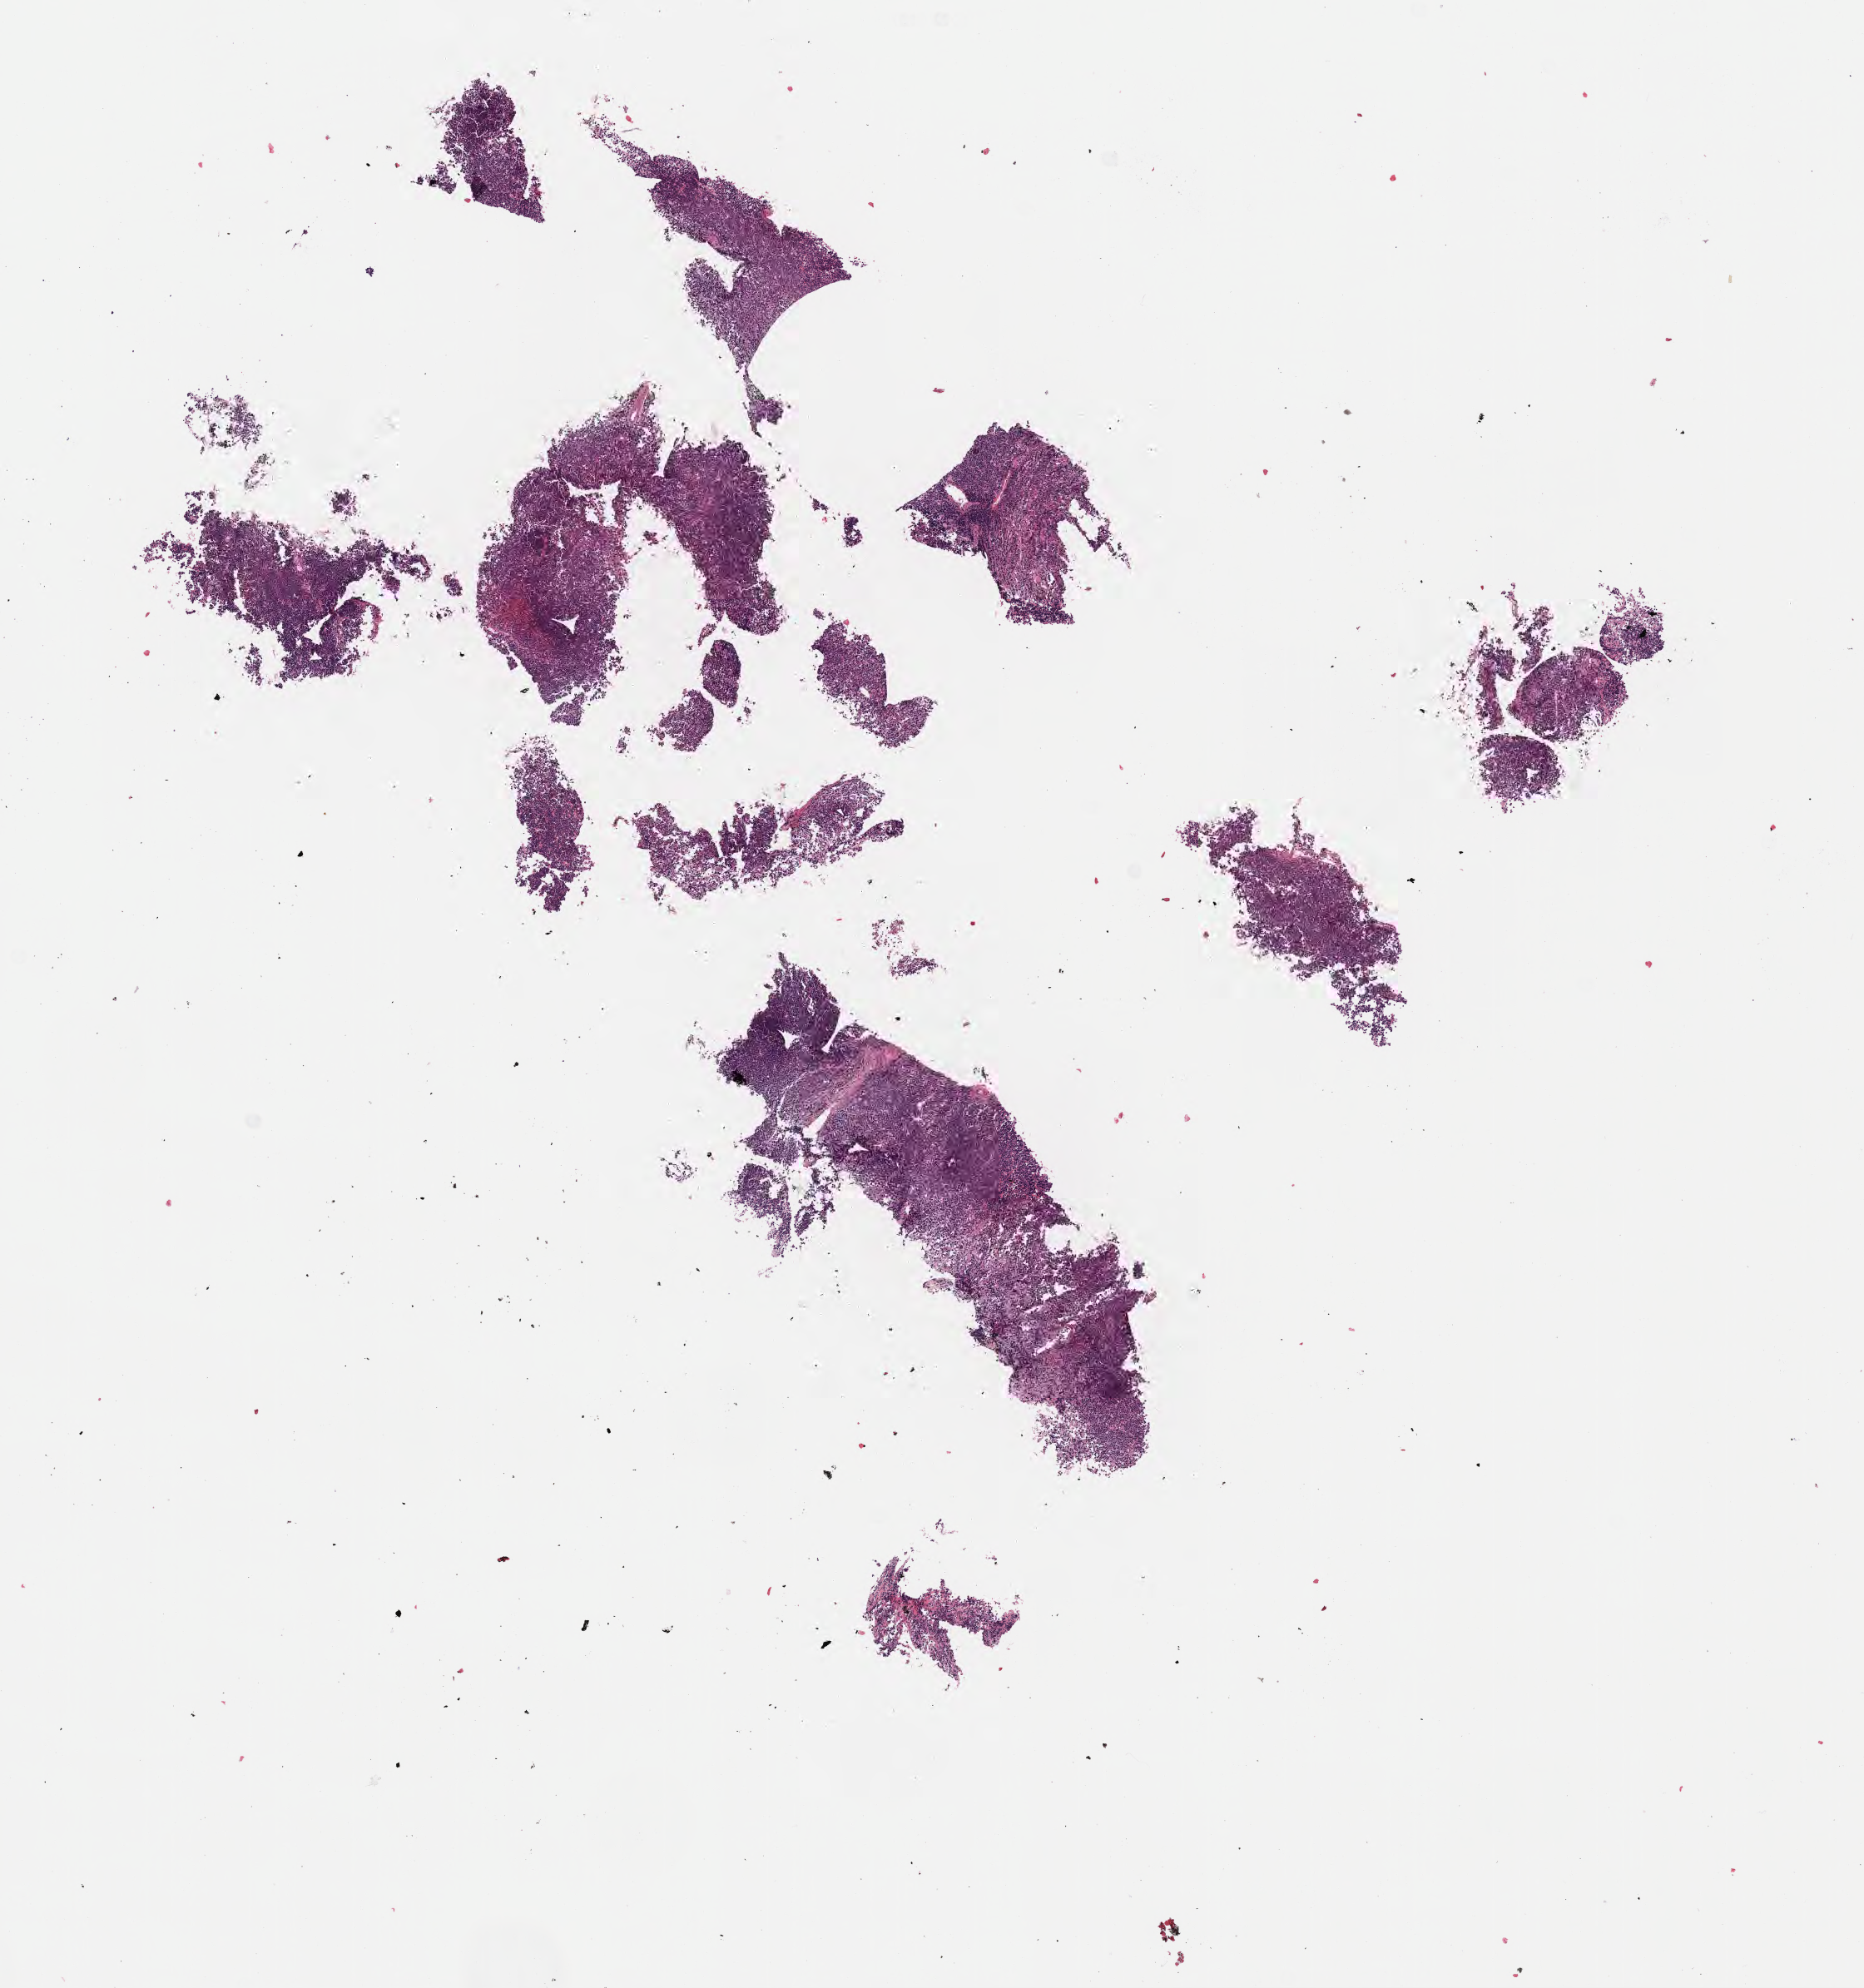
Haematoxylin and eosin whole-slide image, whole scanned area (about 9.1 x 9.7 mm) shown as a low-resolution overview; specimen: tumor tissue; site: kidney. Patient: female, age at initial diagnosis 8 years.
Diagnosis: Burkitt lymphoma, NOS.